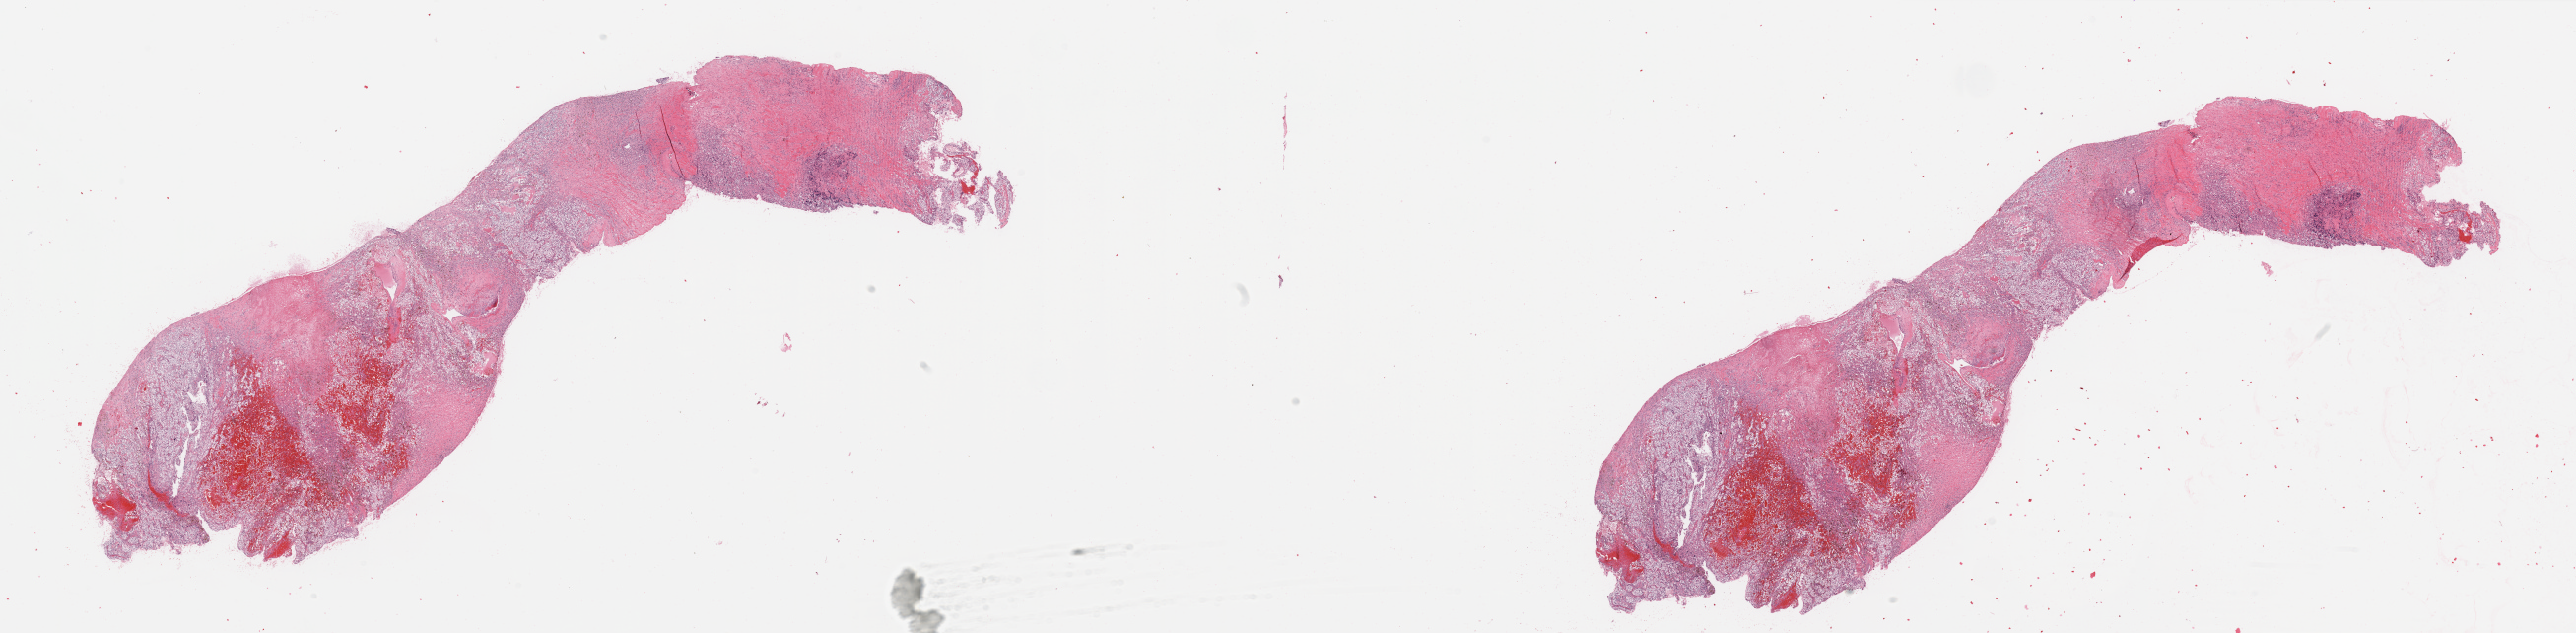
Whole-slide histology image, H&E, a low-resolution overview of the entire scanned area, about 41.3 x 10.2 mm; tumour tissue sample, kidney. 57-year-old male patient. Histologic grade: G3 (poorly differentiated).
AJCC pathologic stage: III. Diagnosis: Renal cell carcinoma, NOS.